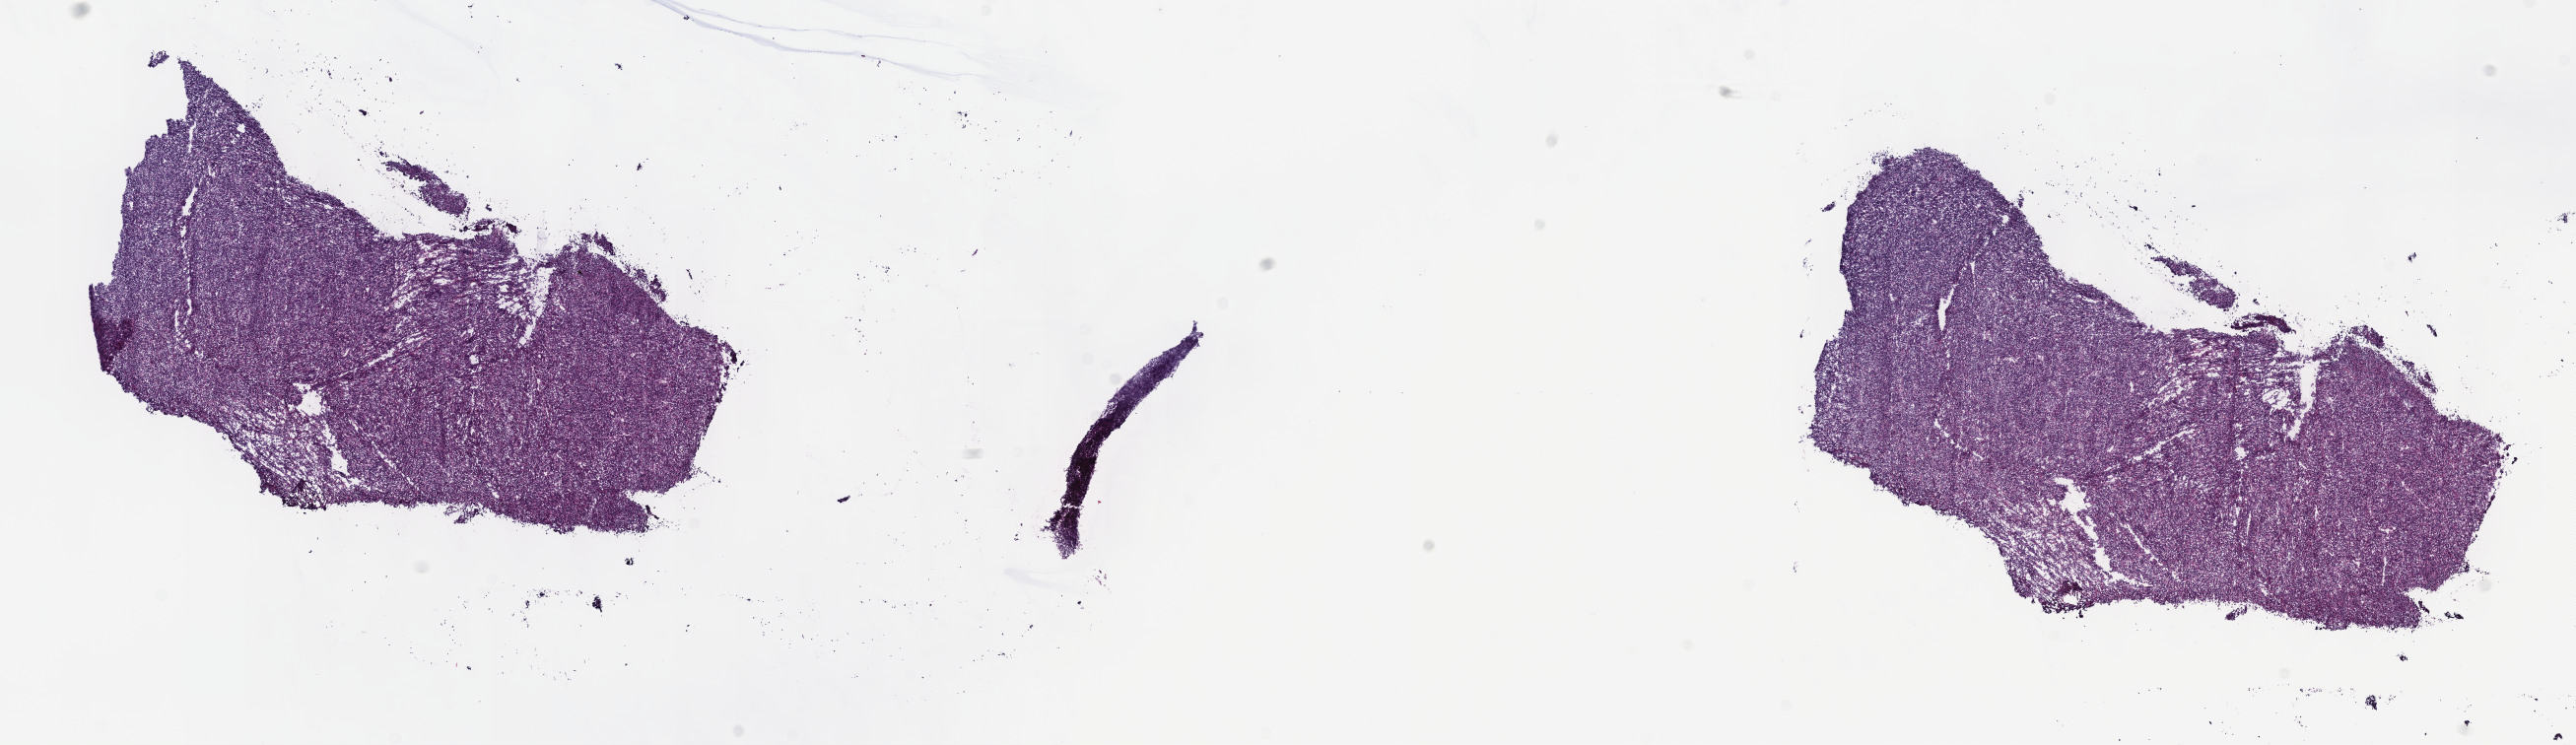
Digitized H&E-stained tissue section (whole slide) — low-resolution overview of the scanned area, about 21.1 x 6.1 mm (acquisition: 40x scan). Frozen section. Sample: primary tumour, connective, subcutaneous and other soft tissues. Patient: female, age at initial diagnosis 31 years. Slide review estimates, as recorded: tumour cells 95%, tumour nuclei 100%, normal cells 0%, stromal cells 5%, necrosis 0%. Infiltration values recorded for this section: lymphocyte infiltration 0%, monocyte infiltration 0%, neutrophil infiltration 0%.
Pathologic diagnosis: Synovial sarcoma, NOS (connective, subcutaneous and other soft tissues of thorax).